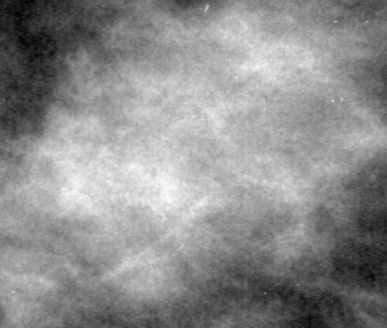
Crop from a digitized film mammogram around one marked abnormality, right breast, MLO view, BI-RADS breast density category 1 (scale 1–4).
Finding: mass, shape lobulated, margins ill defined; BI-RADS assessment category 4; subtlety rating 3 on a 1 (subtle) to 5 (obvious) scale; pathology result (as recorded, not read from the image): benign.